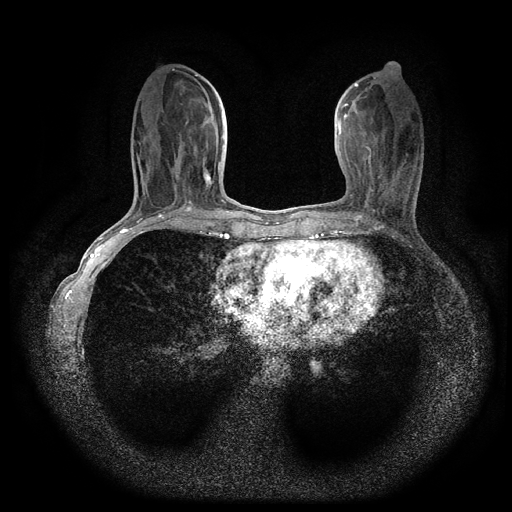
Breast MRI (dynamic contrast-enhanced, multi-phase), one axial slice; position 37 of 116 along the scan axis; dynamic contrast-enhanced series, time point 2 of 5 at this slice position (early post-contrast); 1.5 T; TE 2.7 ms, TR 5.4 ms; 512 × 512 image matrix. Female patient, age 49 years.
Annotated regions visible in this slice (semi-automatically segmented with operator editing):
- breast lesion (labelled benign in the annotation): bounding box [x1, y1, x2, y2] px = [202, 167, 215, 190]